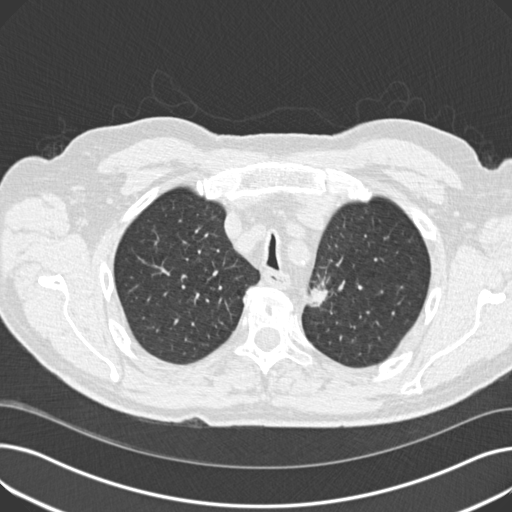
Low-dose screening chest CT, one axial slice. Slice 146 of 191 in the series (ordered by position). Lung window (W 1500 / L -600 HU). 2 mm slice thickness. 512 × 512 image matrix, field of view 370 × 370 mm.
Outlined on this slice (manually delineated by an expert):
- lesion 1 (tumor, upper lobe of left lung): bounding box <308,283,328,307> (left, top, right, bottom; pixels)